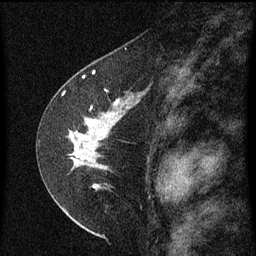
Breast MRI (dynamic contrast-enhanced), one sagittal slice; slice 36 of 60 in the series (ordered by position); dynamic contrast-enhanced series, image 2 of 3 at this slice position (ordered by acquisition); 1.5 T; TE 4.2 ms, TR 8 ms; 2 mm slice thickness; 256 × 256 image matrix, field of view 180 × 180 mm. Female patient, age 47 years.
Annotated regions visible in this slice (semi-automatic segmentation, software-assisted and operator-edited):
- analysis volume of interest (the breast-tissue region the enhancement analysis was run in; not a lesion): bounding box [x1, y1, x2, y2] px = [44, 84, 145, 199]
- tumour enhancement mask (voxels above the 70 % enhancement threshold inside the analysis volume of interest): [70, 100, 127, 189]